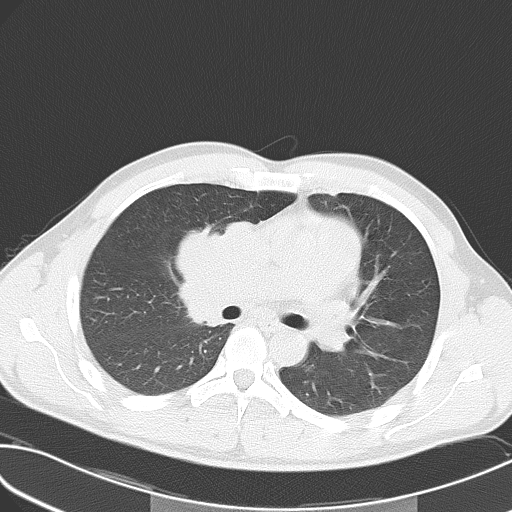
Chest CT, one axial slice; position 33 of 55 along the scan axis; reconstruction kernel B70f; 120 kVp; lung window (W 1500 / L -600 HU); 512 × 512 image matrix, field of view 346 × 346 mm. Male patient, age 32 years. From the clinical record (not read from this slice): clinical TNM (as recorded): T4 N3 M0; histopathological grade: G3.
Outlined on this slice (rectangle marked by the reading radiologist):
- lung tumour (recorded histology: small cell carcinoma): bounding box (x1, y1, x2, y2) in pixels: (171, 211, 257, 328)